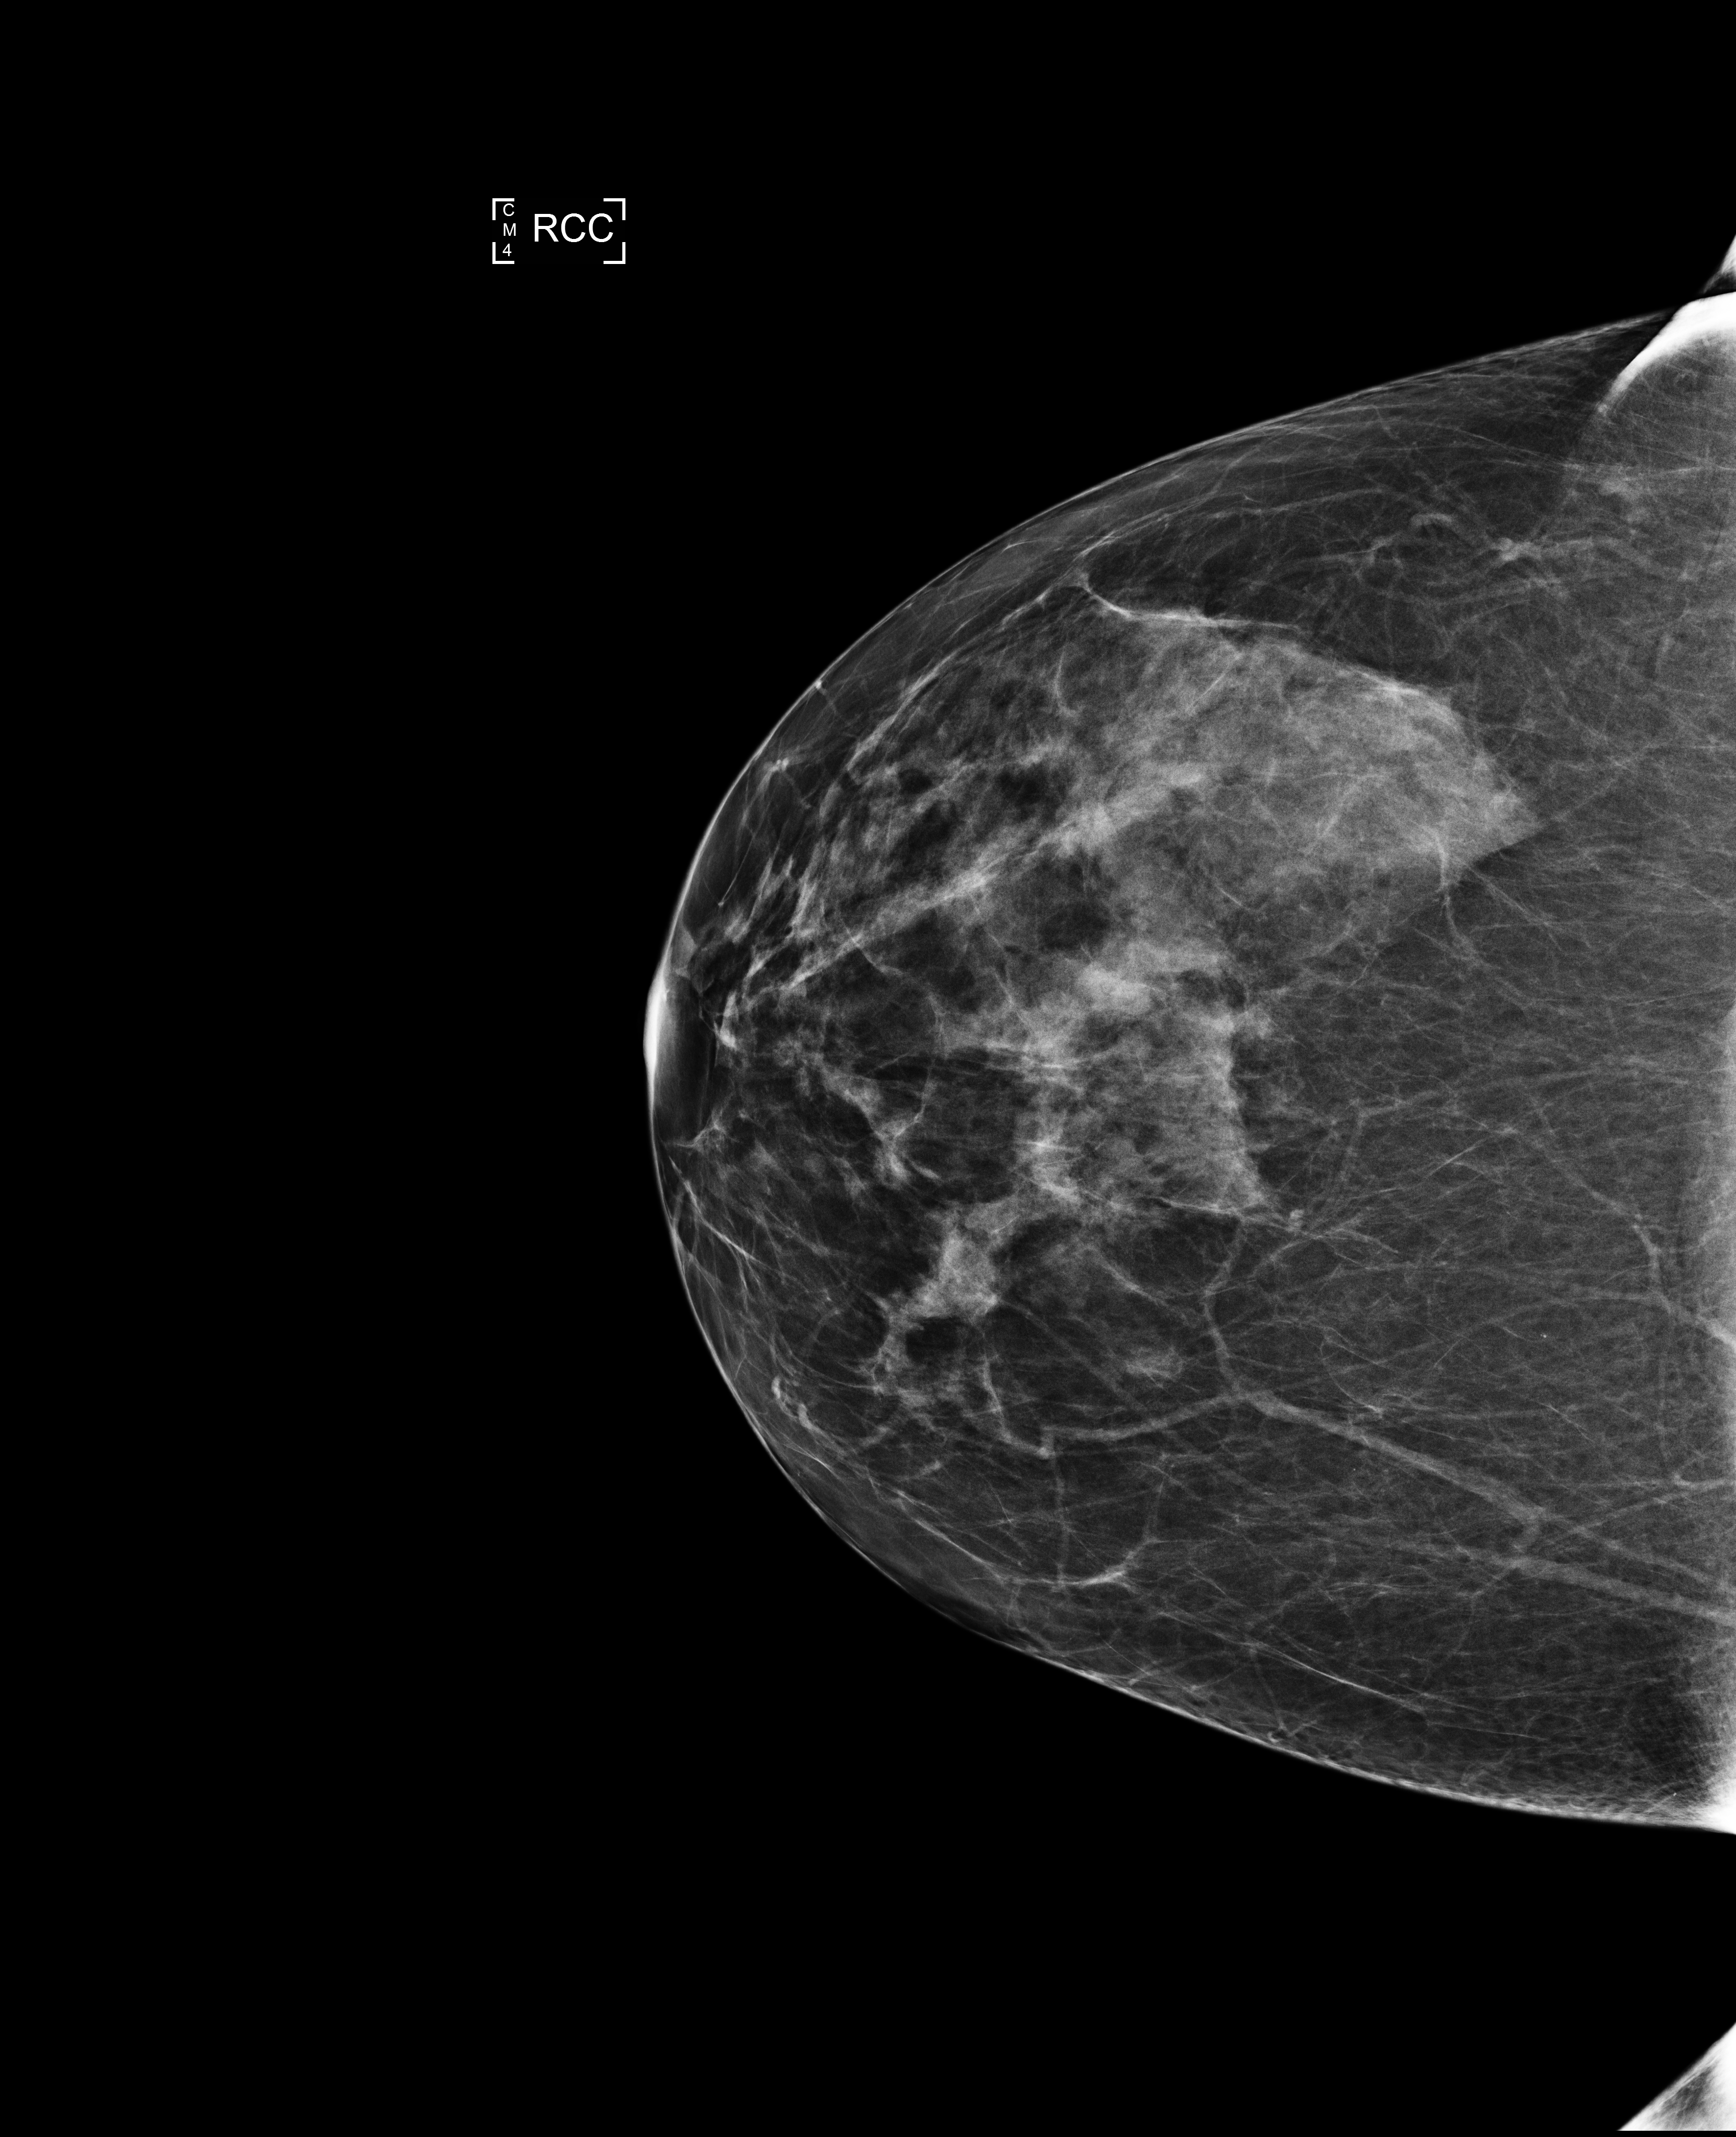
Full-field digital mammogram (FFDM); right breast; CC view; screening examination. Patient aged 55 years (female).
- breast density at the screening exam (both breasts): heterogeneously dense (BI-RADS density category c)
- final BI-RADS assessment for this screening round (tomosynthesis exam, both breasts): category 1
- recall: no recall after this screen